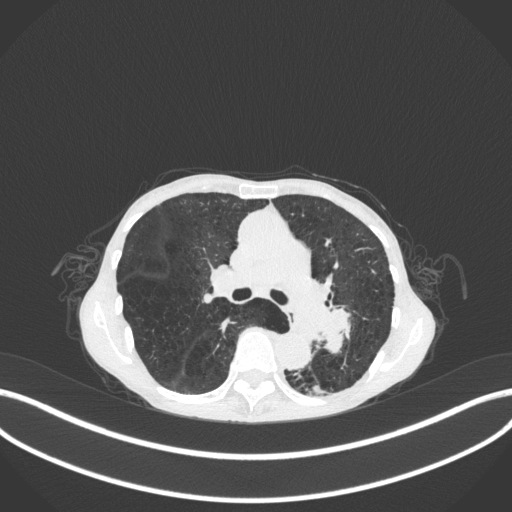
Chest CT, one axial slice; reconstruction kernel B31f; 120 kVp; lung window (W 1500 / L -600 HU); 1 mm slice thickness; 512 × 512 image matrix, field of view 400 × 400 mm. Patient: female, 70 years. From the clinical record (not read from this slice): clinical TNM (as recorded): T3 N0 M0.
Annotated regions visible in this slice (rectangle marked by the reading radiologist):
- lung tumour (recorded histology: small cell carcinoma): box from (x=310, y=287) to (x=369, y=364) px